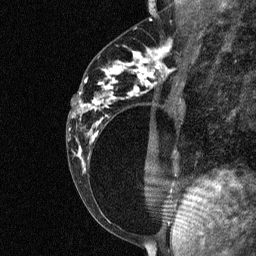
Breast MRI (dynamic contrast-enhanced), one sagittal slice; slice 30 of 64 in the series (ordered by position); dynamic contrast-enhanced study with each time point stored as its own series, time point 2 of 3 at this slice position (early post-contrast, ordered by acquisition time); 1.5 T; TE 4.8 ms, TR 27 ms; 2 mm slice thickness; 256 × 256 image matrix. Female patient, age 34 years. Case-level facts recorded for this patient, not image findings: setting: breast cancer imaged before/during neoadjuvant chemotherapy; receptor status: HR-positive, HER2-negative.
Structures marked on this image (semi-automatic segmentation, software-assisted and operator-edited):
- analysis volume of interest (the breast-tissue region the enhancement analysis was run in; not a lesion): bounding box [x1, y1, x2, y2] px = [78, 44, 181, 191]
- tumour enhancement mask (voxels above the 90 % enhancement threshold inside the analysis volume of interest): [157, 48, 164, 68]